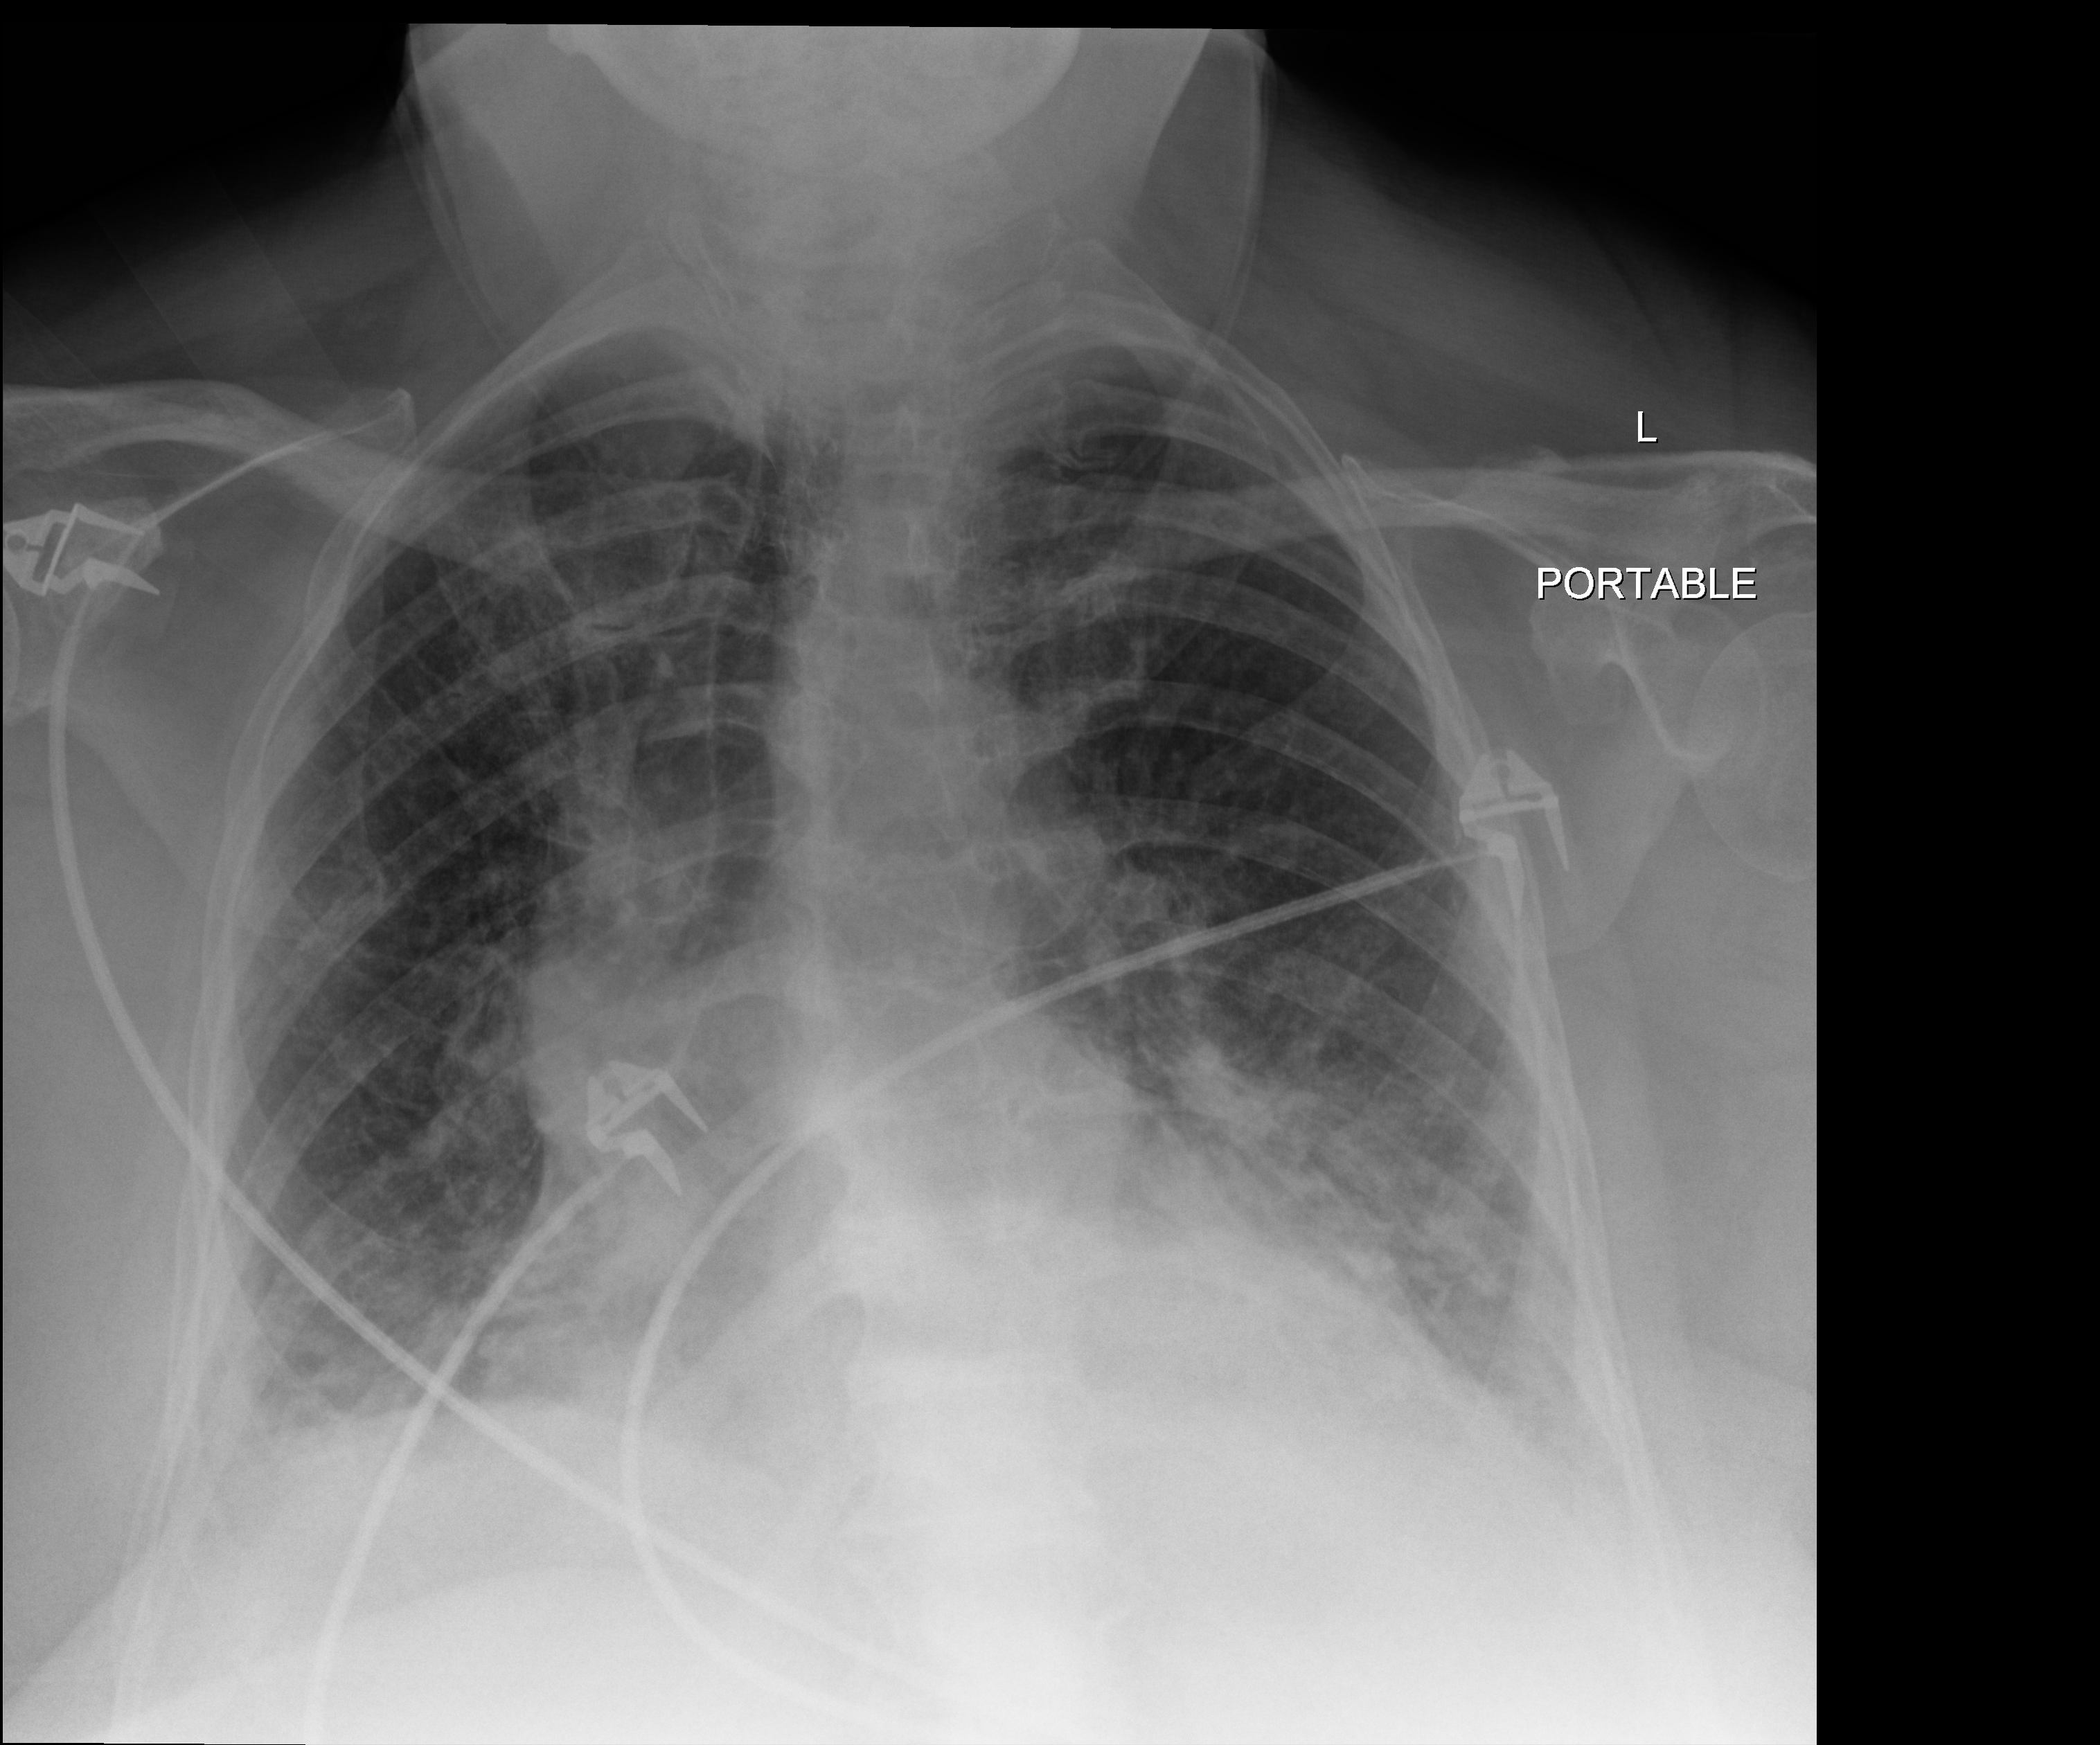
Chest radiograph; anteroposterior (AP) projection. Female patient hospitalised with COVID-19, age 75–90 years.
Hospital-stay facts (about this admission, not read from this image; timing relative to this image not recorded): mechanically ventilated during this hospital stay: no.